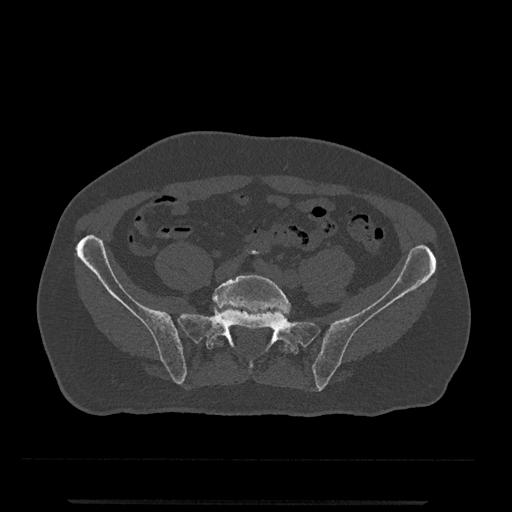
CT including the spine, one axial slice; slice 37 of 797 in the series (ordered by position); reconstruction kernel Br40s/3; 120 kVp; bone window (W 1800 / L 400 HU); 512 × 512 image matrix, field of view 419 × 419 mm. Male patient, age 63 years. From the clinical record (not read from this slice): primary cancer: prostate.
Outlined on this slice (semi-automatically segmented with operator editing):
- L5 vertebra: bounding box [x1, y1, x2, y2] px = [209, 274, 291, 352]